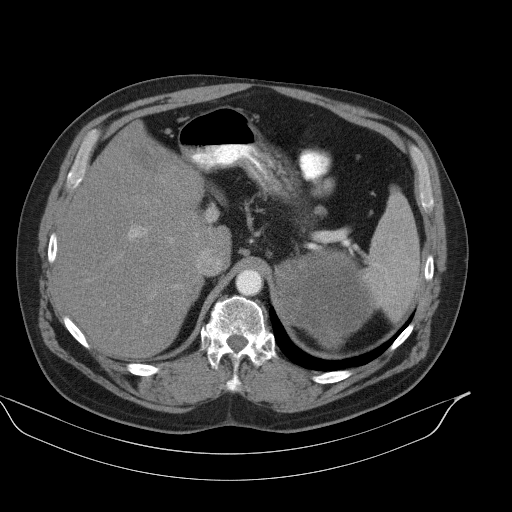
Contrast-enhanced abdominal CT, one axial slice; slice 73 of 92 in the series (ordered by position); reconstruction kernel B41s; 130 kVp; intravenous contrast given; soft-tissue window (W 400 / L 40 HU); 5 mm slice thickness; 512 × 512 image matrix. Male patient, age 56 years. Case-level facts recorded for this patient, not image findings: diagnosis: adrenocortical carcinoma; tumour side: left adrenal; tumour size at pathology: 15 cm; Ki-67 index: 35 %; stage (as recorded): 4.
Annotated regions visible in this slice (semi-automatic segmentation, software-assisted and operator-edited):
- mass: bounding box [x1, y1, x2, y2] px = [277, 249, 373, 348]